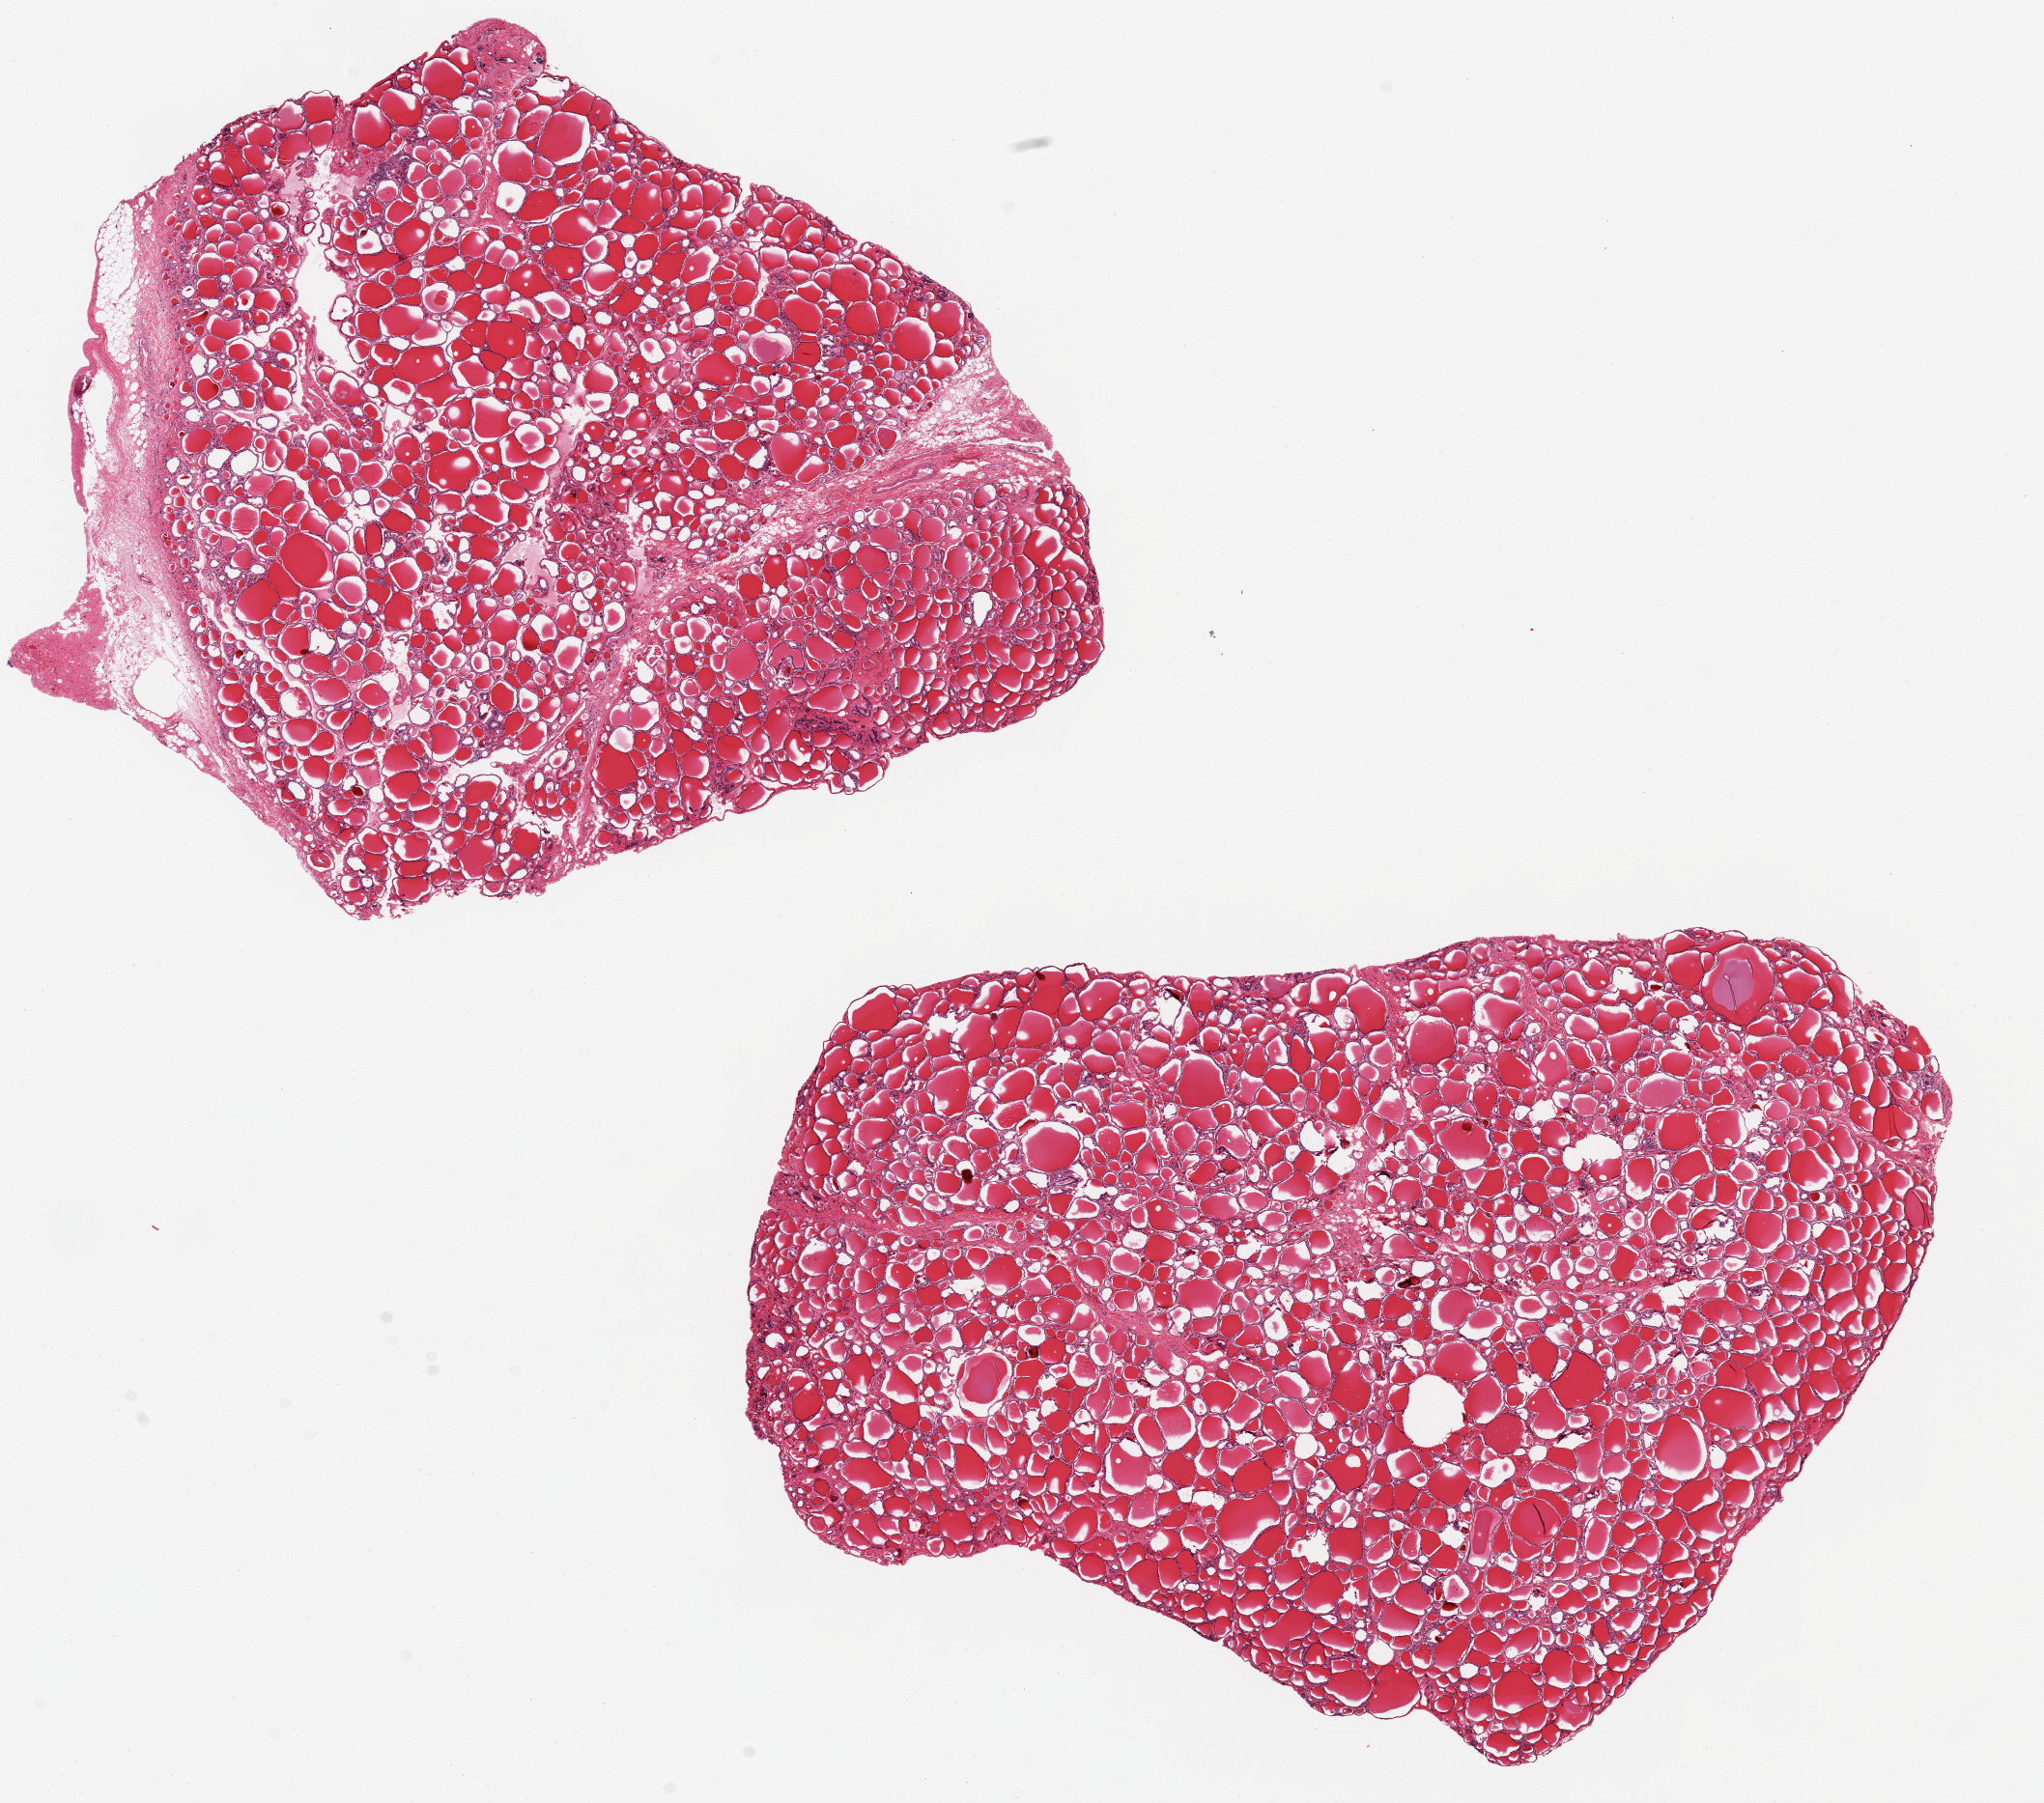
Digitized H&E-stained section — shown as a low-resolution overview of the whole scanned area (about 16.7 x 14.8 mm, acquisition: 20x scan), PAXgene-fixed, paraffin-embedded tissue, target tissue: thyroid, tissue donor sample.
Pathologist's review note for this sample: 2 ~8x6.5mm aliquots.